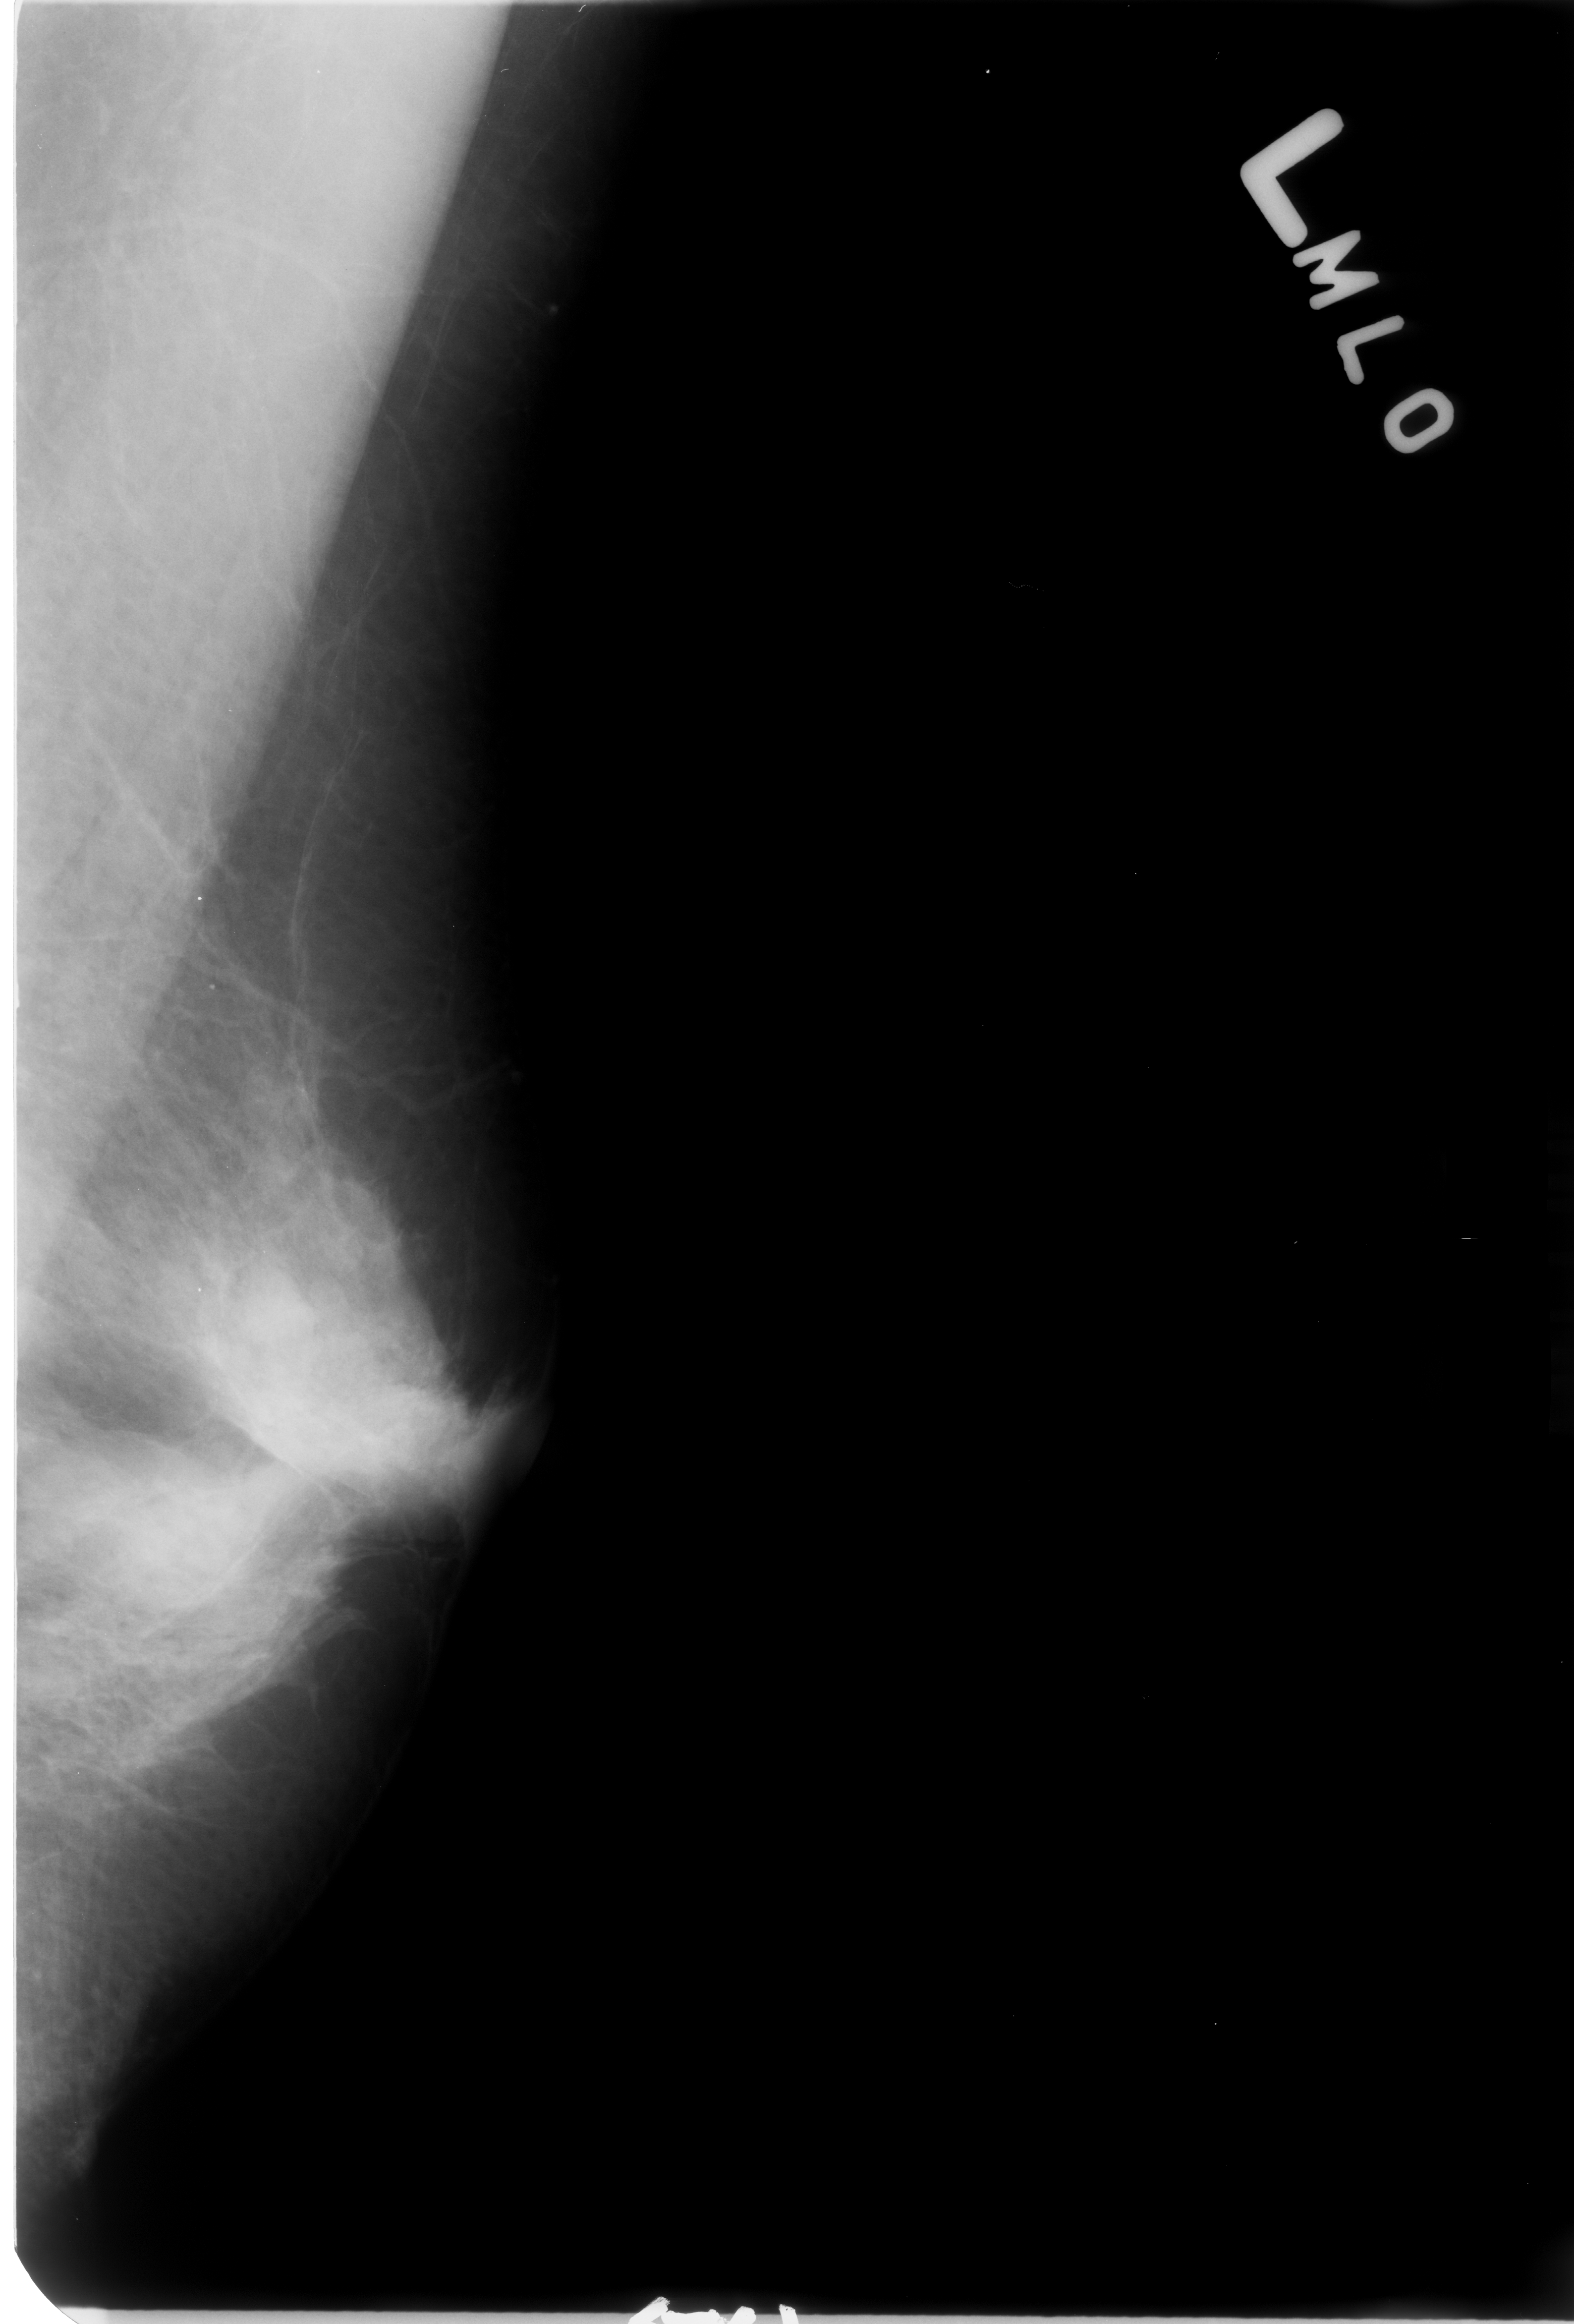
Scanned film-screen mammogram. Left breast. MLO view. BI-RADS breast density category 3 (scale 1–4). 1574 × 2324 image matrix.
Expert-marked regions of interest on this film, with their recorded descriptors:
- mass, shape architectural distortion, margins ill defined; BI-RADS assessment category 3; subtlety rating 3 on a 1 (subtle) to 5 (obvious) scale; outcome (as recorded, no biopsy): benign without callback (not worked up further): bounding box <182,1273,457,1564> (left, top, right, bottom; pixels)